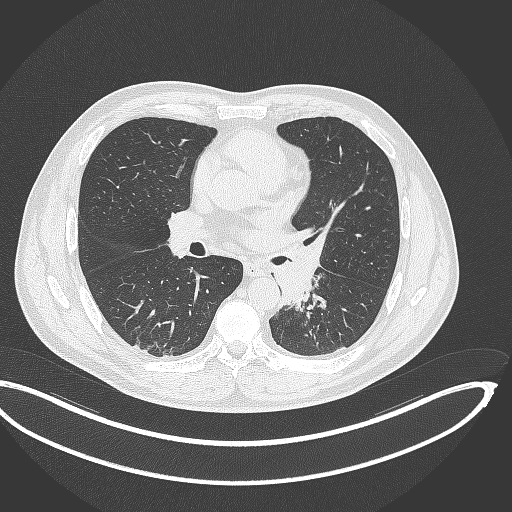
Chest CT, one axial slice. Slice 190 of 362 in the series (ordered by position). 120 kVp. Lung window (W 1500 / L -600 HU). 1 mm slice thickness. 512 × 512 image matrix, field of view 442 × 442 mm. Patient: male, 50 years. From the clinical record (not read from this slice): clinical TNM (as recorded): T2a N3 M0.
Outlined on this slice (bounding box drawn by a radiologist):
- lung tumour (recorded histology: squamous cell carcinoma): bounding box [x1, y1, x2, y2] px = [263, 231, 327, 309]